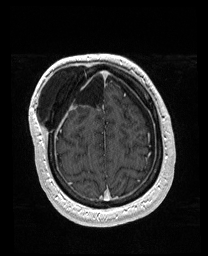
Brain MRI from a brain-tumour surgery series, one axial slice; slice 45 of 176 in the series (ordered by position); T1-weighted post-contrast; 1 mm slice thickness; 208 × 256 image matrix, field of view 208 × 256 mm. Case-level facts recorded for this patient, not image findings: histopathology: Astrocytoma; WHO grade: 4; IDH mutation: yes.
Annotated regions visible in this slice (manually delineated by an expert):
- previous resection cavity: bounding box (x1, y1, x2, y2) in pixels: (56, 69, 106, 107)